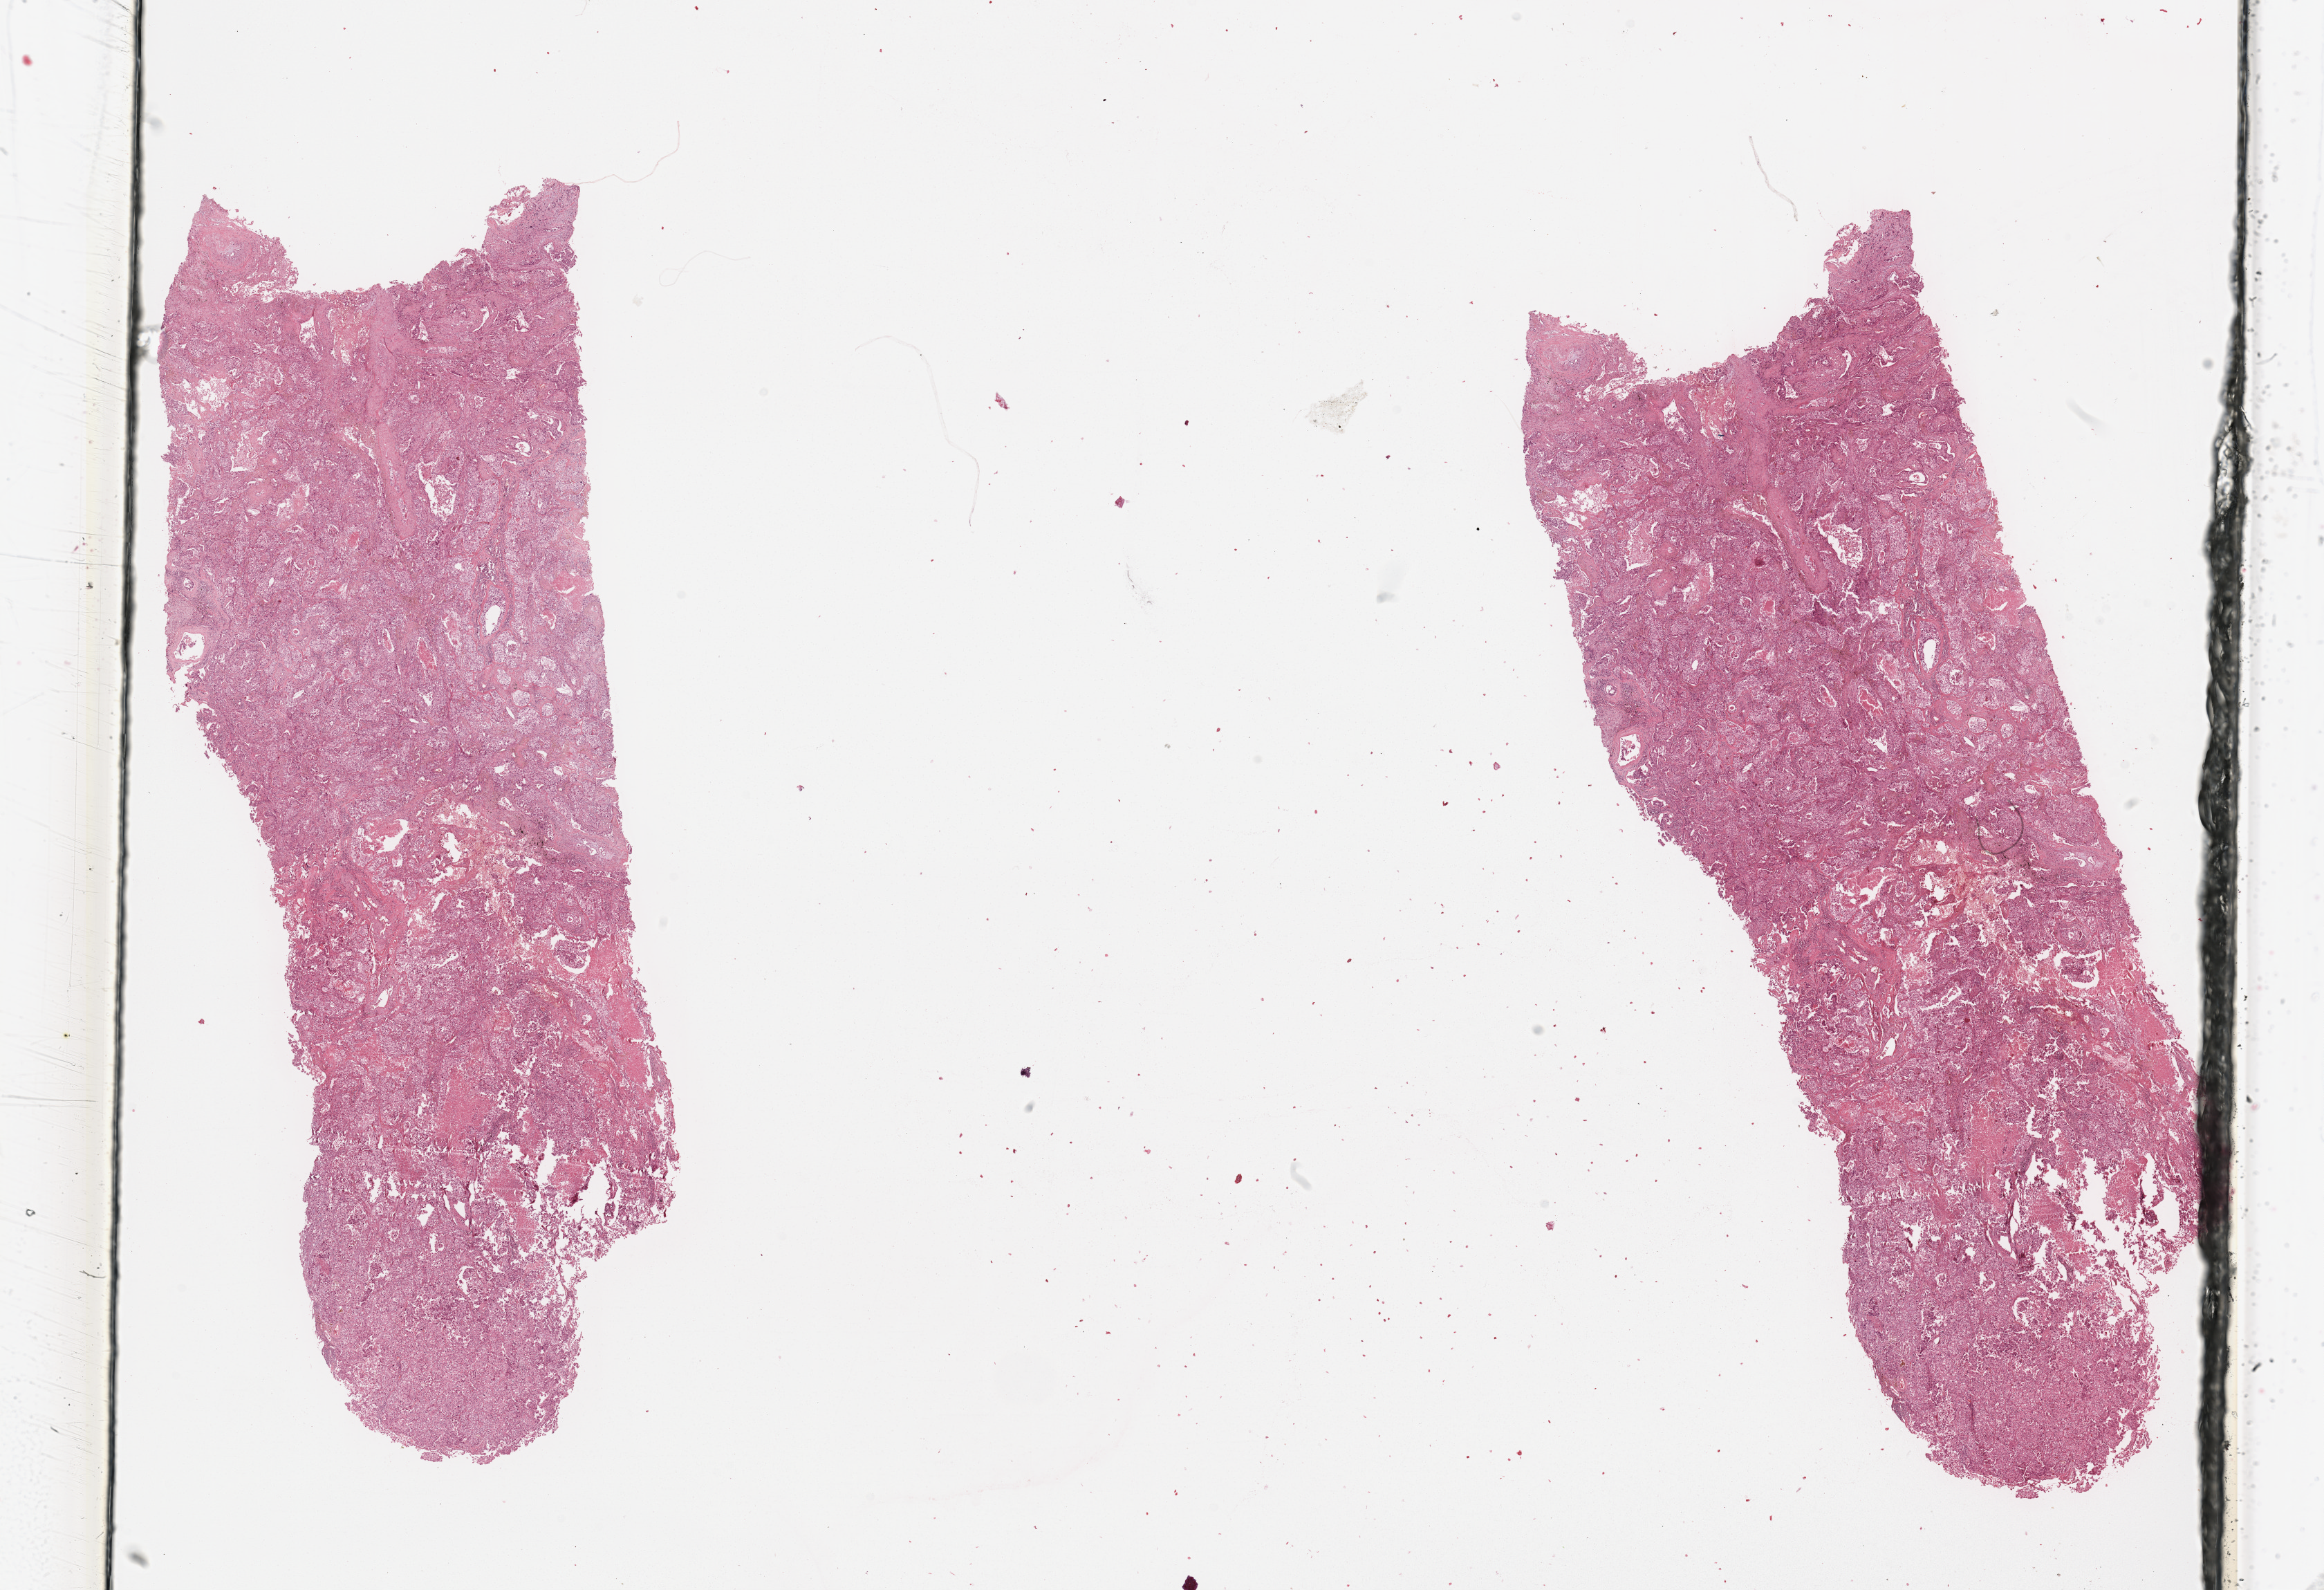
Digitized H&E tissue section (whole slide), whole scanned area (about 26.6 x 18.2 mm, slide scanned at 20x) shown as a low-resolution overview; tumour tissue sample, sampled site: lung. Patient: male, age 72 years. Histologic grade: G2 (moderately differentiated). Pathologist review of this section (percent, as recorded): tumour nuclei 70%, necrosis 10%.
AJCC pathologic stage: IB. Primary tumour site (as recorded): left lower lobe. Diagnosis: Adenocarcinoma, NOS.